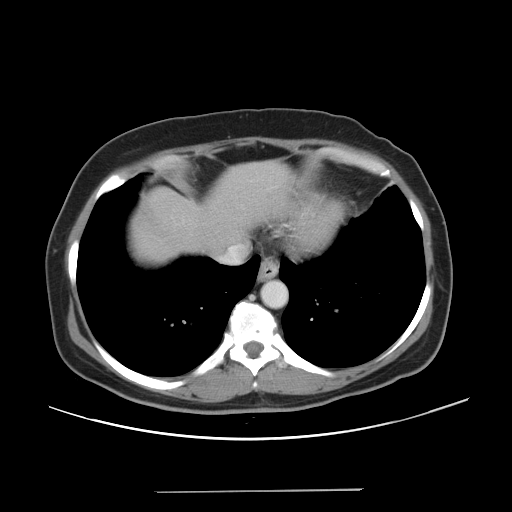
Contrast-enhanced abdominal CT, one axial slice. Slice 43 of 56 in the series (ordered by position). 120 kVp. Intravenous contrast given. Soft-tissue window (W 400 / L 40 HU). 5 mm slice thickness. 512 × 512 image matrix, field of view 419 × 419 mm. Female patient, age 54 years. Case-level facts recorded for this patient, not image findings: diagnosis: colorectal cancer liver metastases, imaged before liver resection; multiple liver metastases: yes; largest metastasis: 3.2 cm; disease in both lobes: yes.
Annotated regions visible in this slice (outlined manually by an expert reader):
- liver: bounding box [x1, y1, x2, y2] px = [135, 163, 291, 261]
- planned liver remnant (the part of the liver to remain after resection): [214, 163, 293, 242]